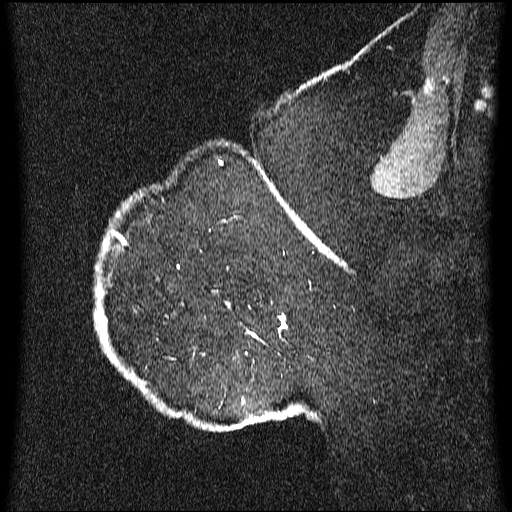
Breast MRI (dynamic contrast-enhanced), one sagittal slice. Position 49 of 64 along the scan axis. Dynamic contrast-enhanced series, image 2 of 3 at this slice position (ordered by acquisition). 1.5 T. TE 4.2 ms, TR 9.1 ms. 512 × 512 image matrix, field of view 180 × 180 mm. Female patient, age 52 years.
Outlined on this slice (semi-automatic segmentation, software-assisted and operator-edited):
- analysis volume of interest (the breast-tissue region the enhancement analysis was run in; not a lesion): bounding box (x1, y1, x2, y2) in pixels: (95, 203, 350, 433)
- tumour enhancement mask (voxels above the 70 % enhancement threshold inside the analysis volume of interest): (96, 203, 345, 429)